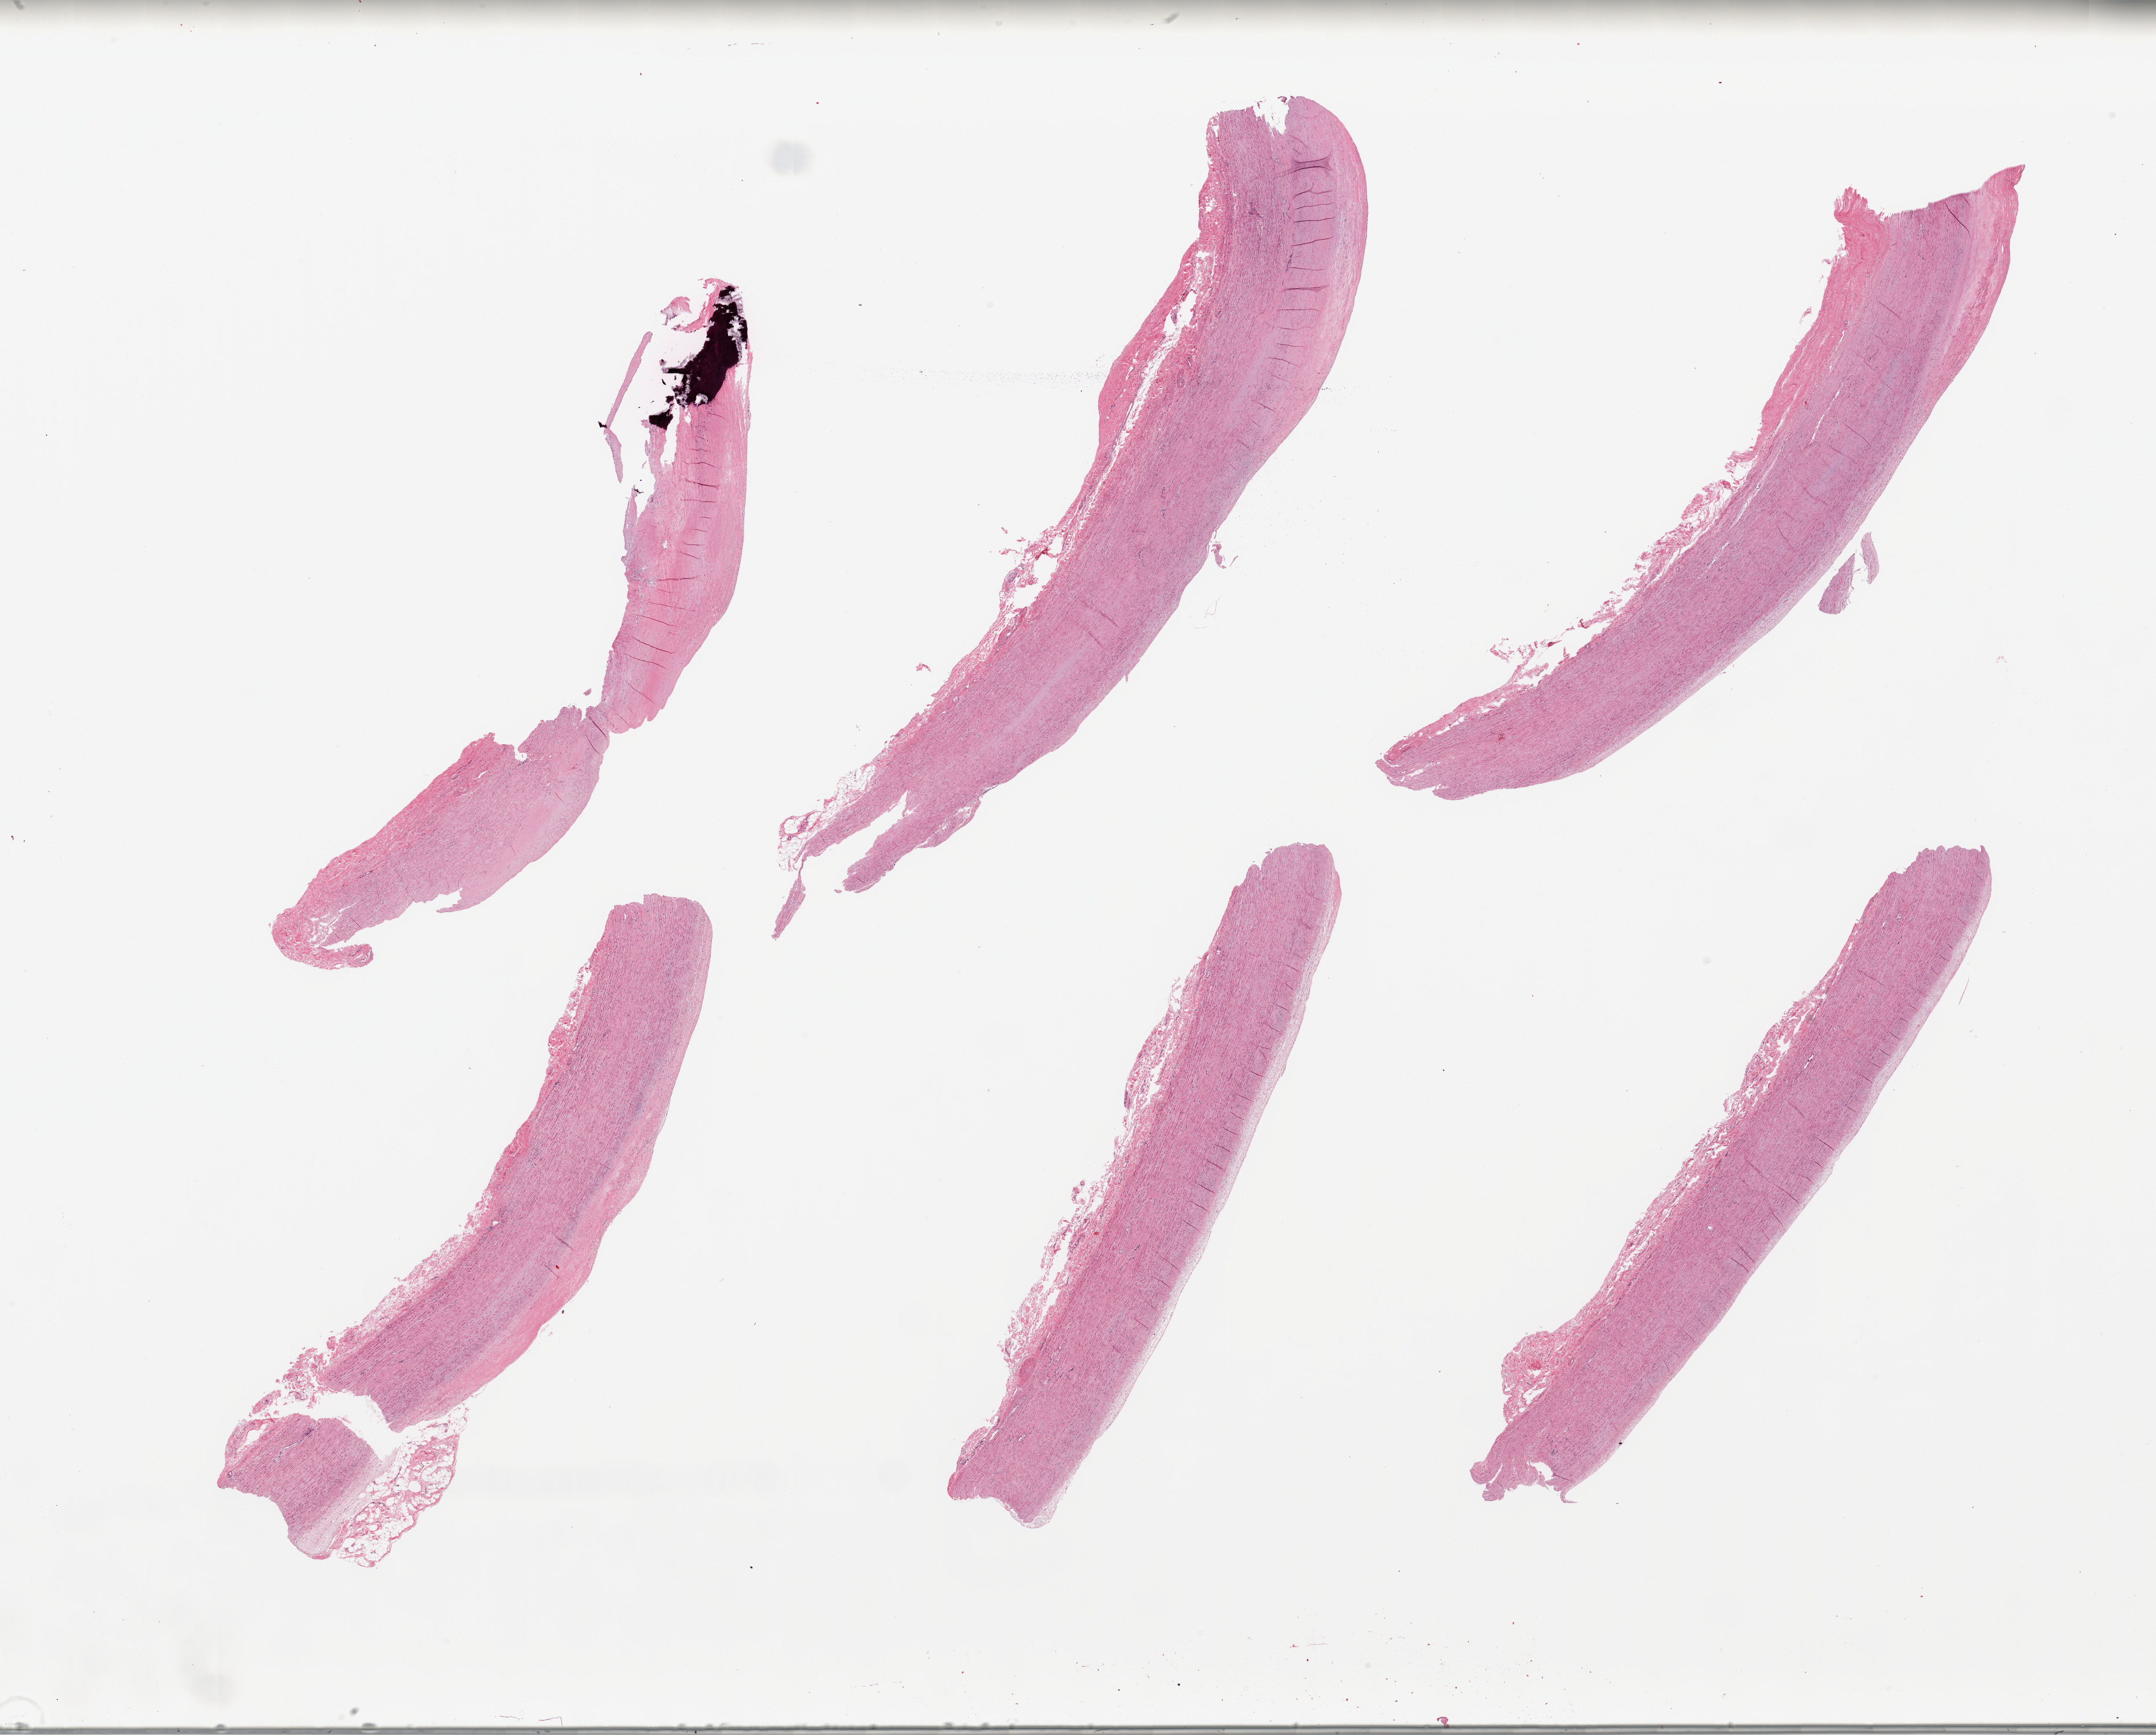
Digitized haematoxylin and eosin-stained section — shown as a low-resolution overview of the whole scanned area (about 29.5 x 23.8 mm). PAXgene-fixed paraffin-embedded (PFPE) section. Section of aorta (target tissue). Donor tissue sample.
- pathologist's review note for this sample: 6 pieces; slight linear plaques; 1.8mm calcification